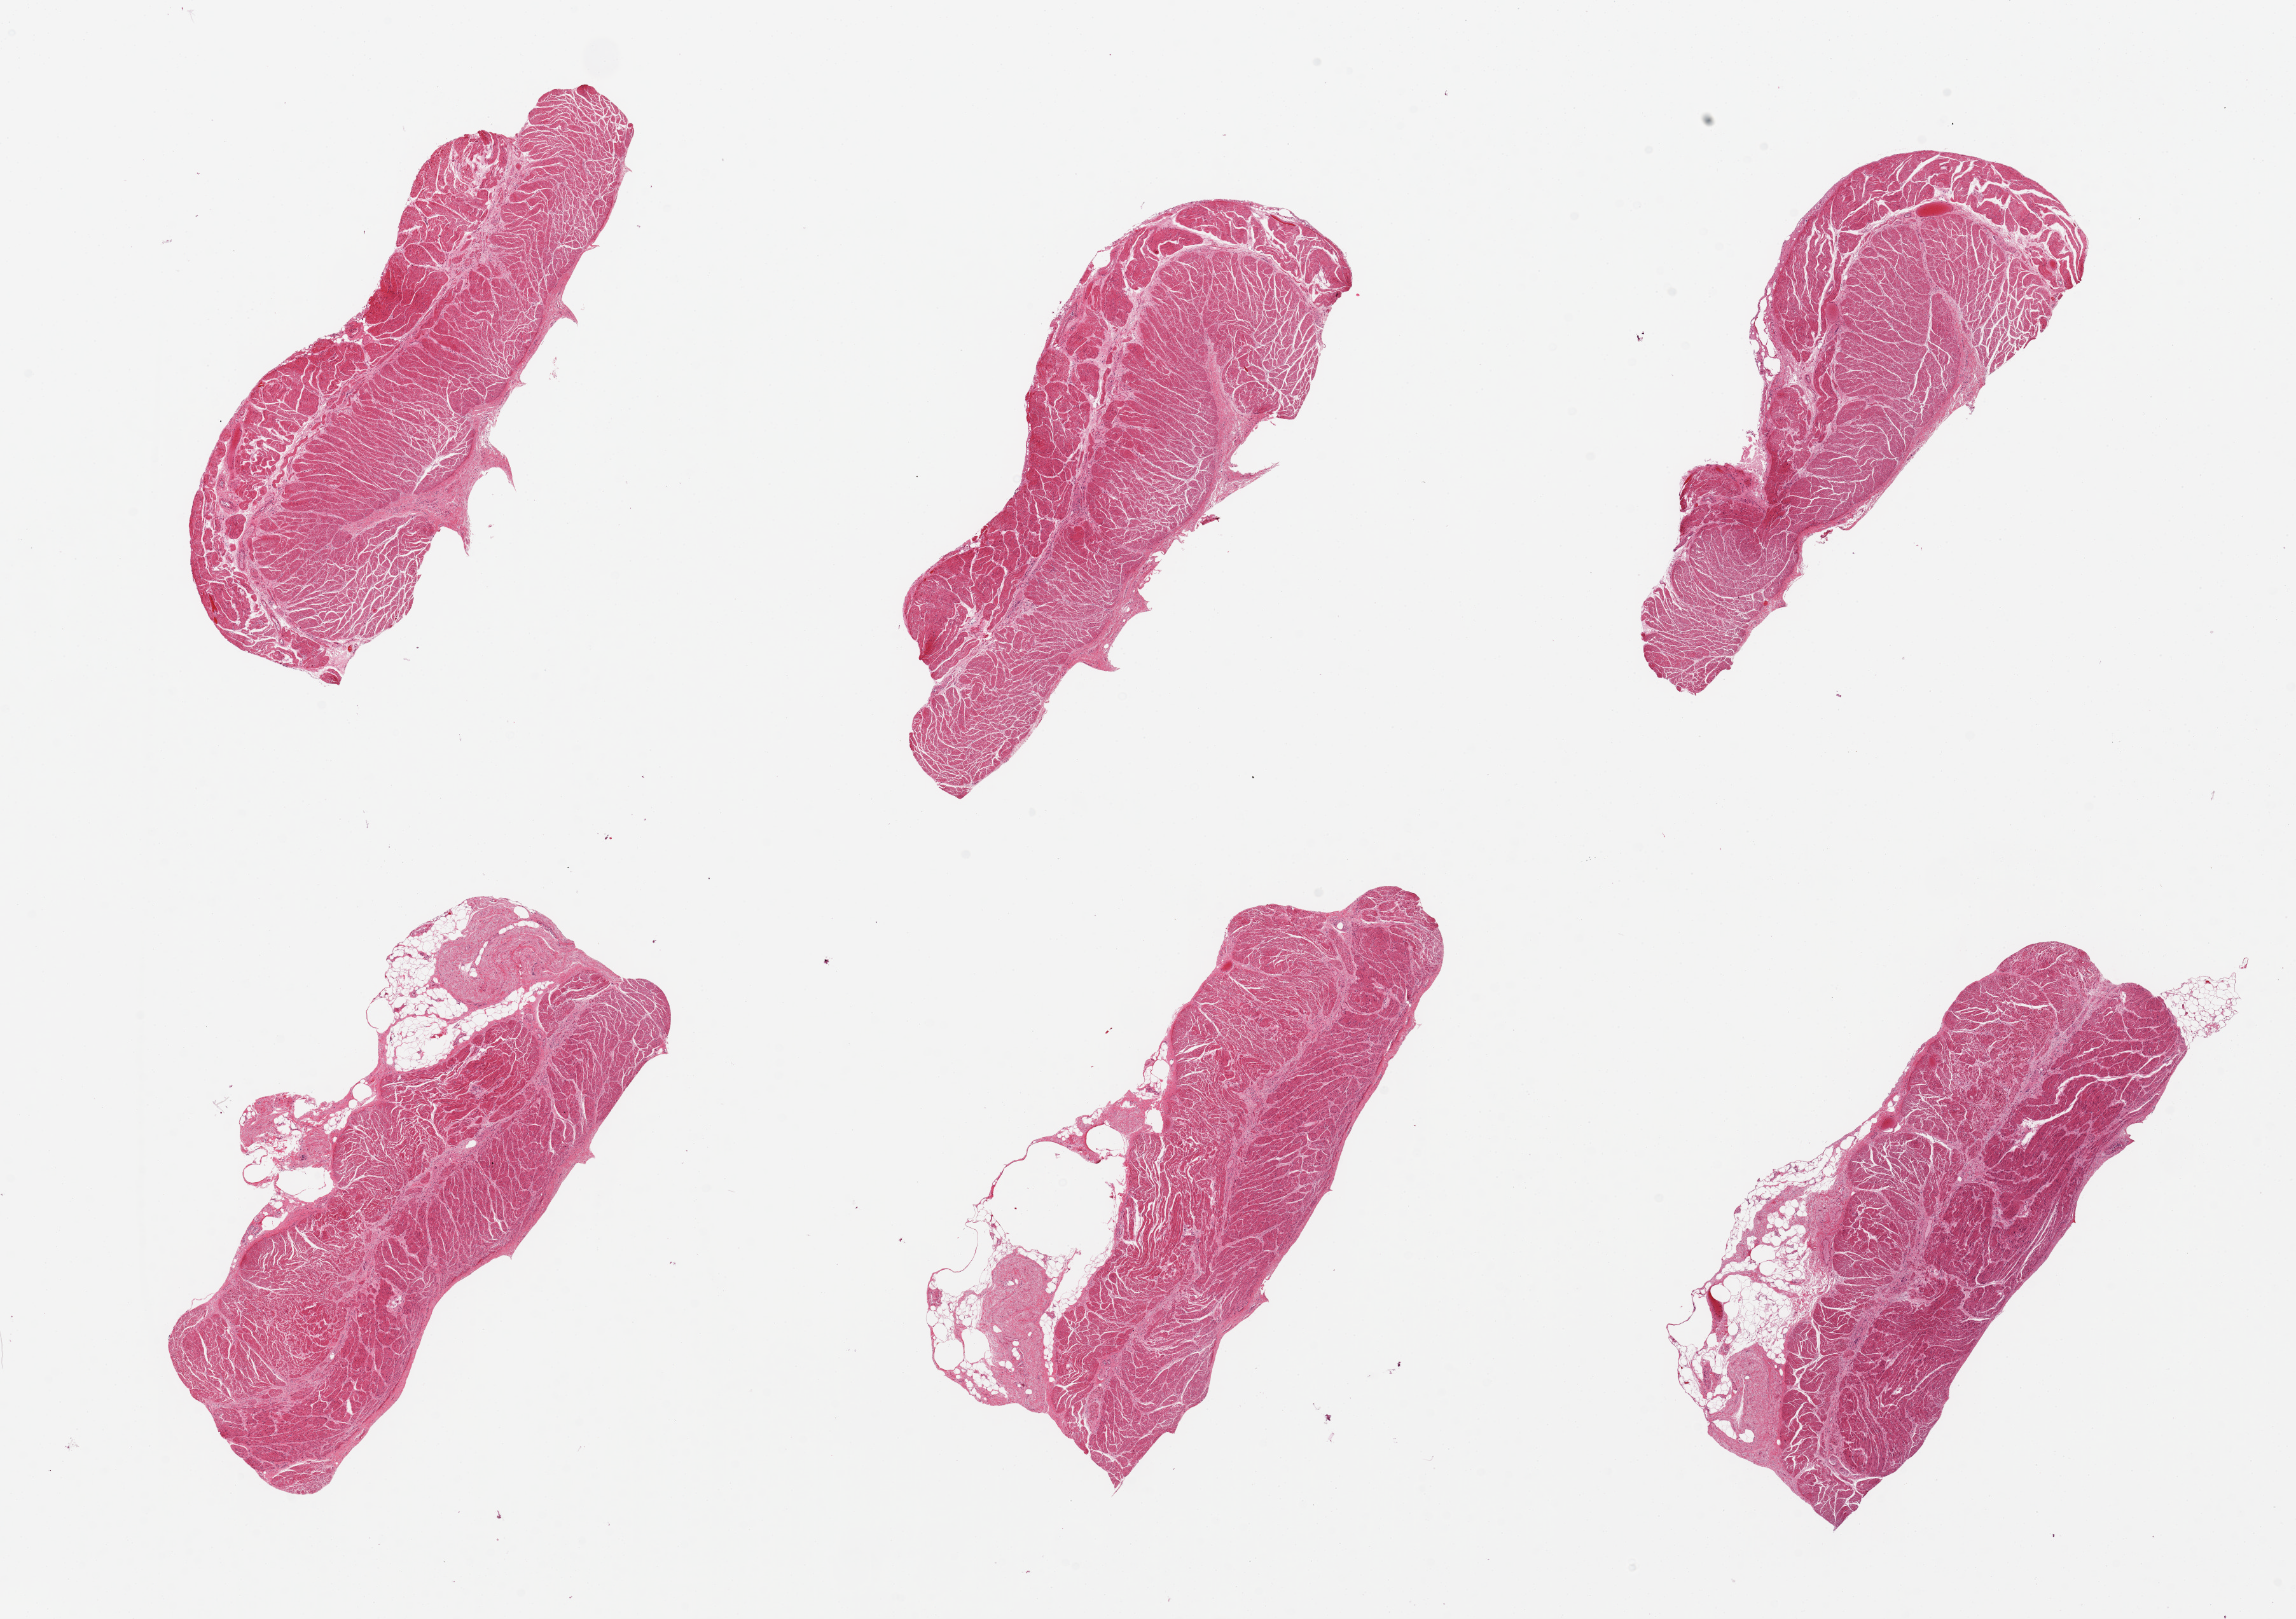
Digitized hematoxylin and eosin (H&E)-stained section, brightfield — whole scanned area (about 28.5 x 20.1 mm) shown as a low-resolution overview, PAXgene-fixed paraffin-embedded (PFPE) section, section of gastroesophageal junction (target tissue), tissue donor sample. Donor: female.
- reviewer comment on this tissue sample: 6 pieces, musuclaris, nubbins of adherent fat on 3